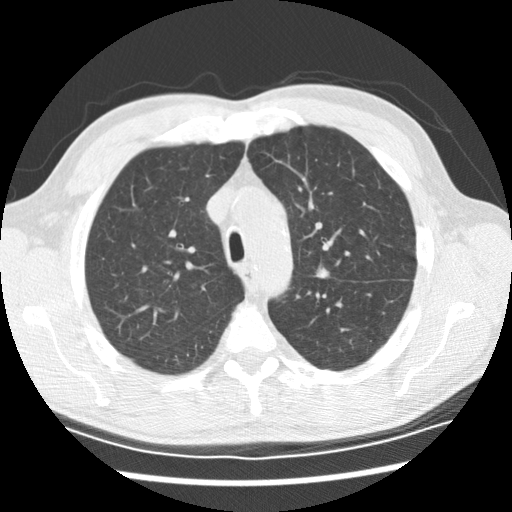
Low-dose screening chest CT, axial slice, second screening round (one year after baseline), lung window (W 1500 / L -600 HU), slice 58 of 208 in the series. Male, age 59 years at enrolment. Current smoker at enrolment.
- Expert-annotated lung lesion, bounding box <305,259,341,293> (left, top, right, bottom; pixels).
- Screening reader's record for this exam (one nodule recorded; not confirmed to be the boxed lesion): non-calcified nodule or mass ≥4 mm, left upper lobe, 8 × 7 mm, spiculated (stellate) margins, soft tissue attenuation, pre-existing on the prior screen: yes; interval growth: yes.
- Later outcome: lung cancer diagnosed 251 days after this screen — adenocarcinoma, NOS, left upper lobe, left lower lobe, poorly differentiated (G3), stage IV (AJCC 6th edition).